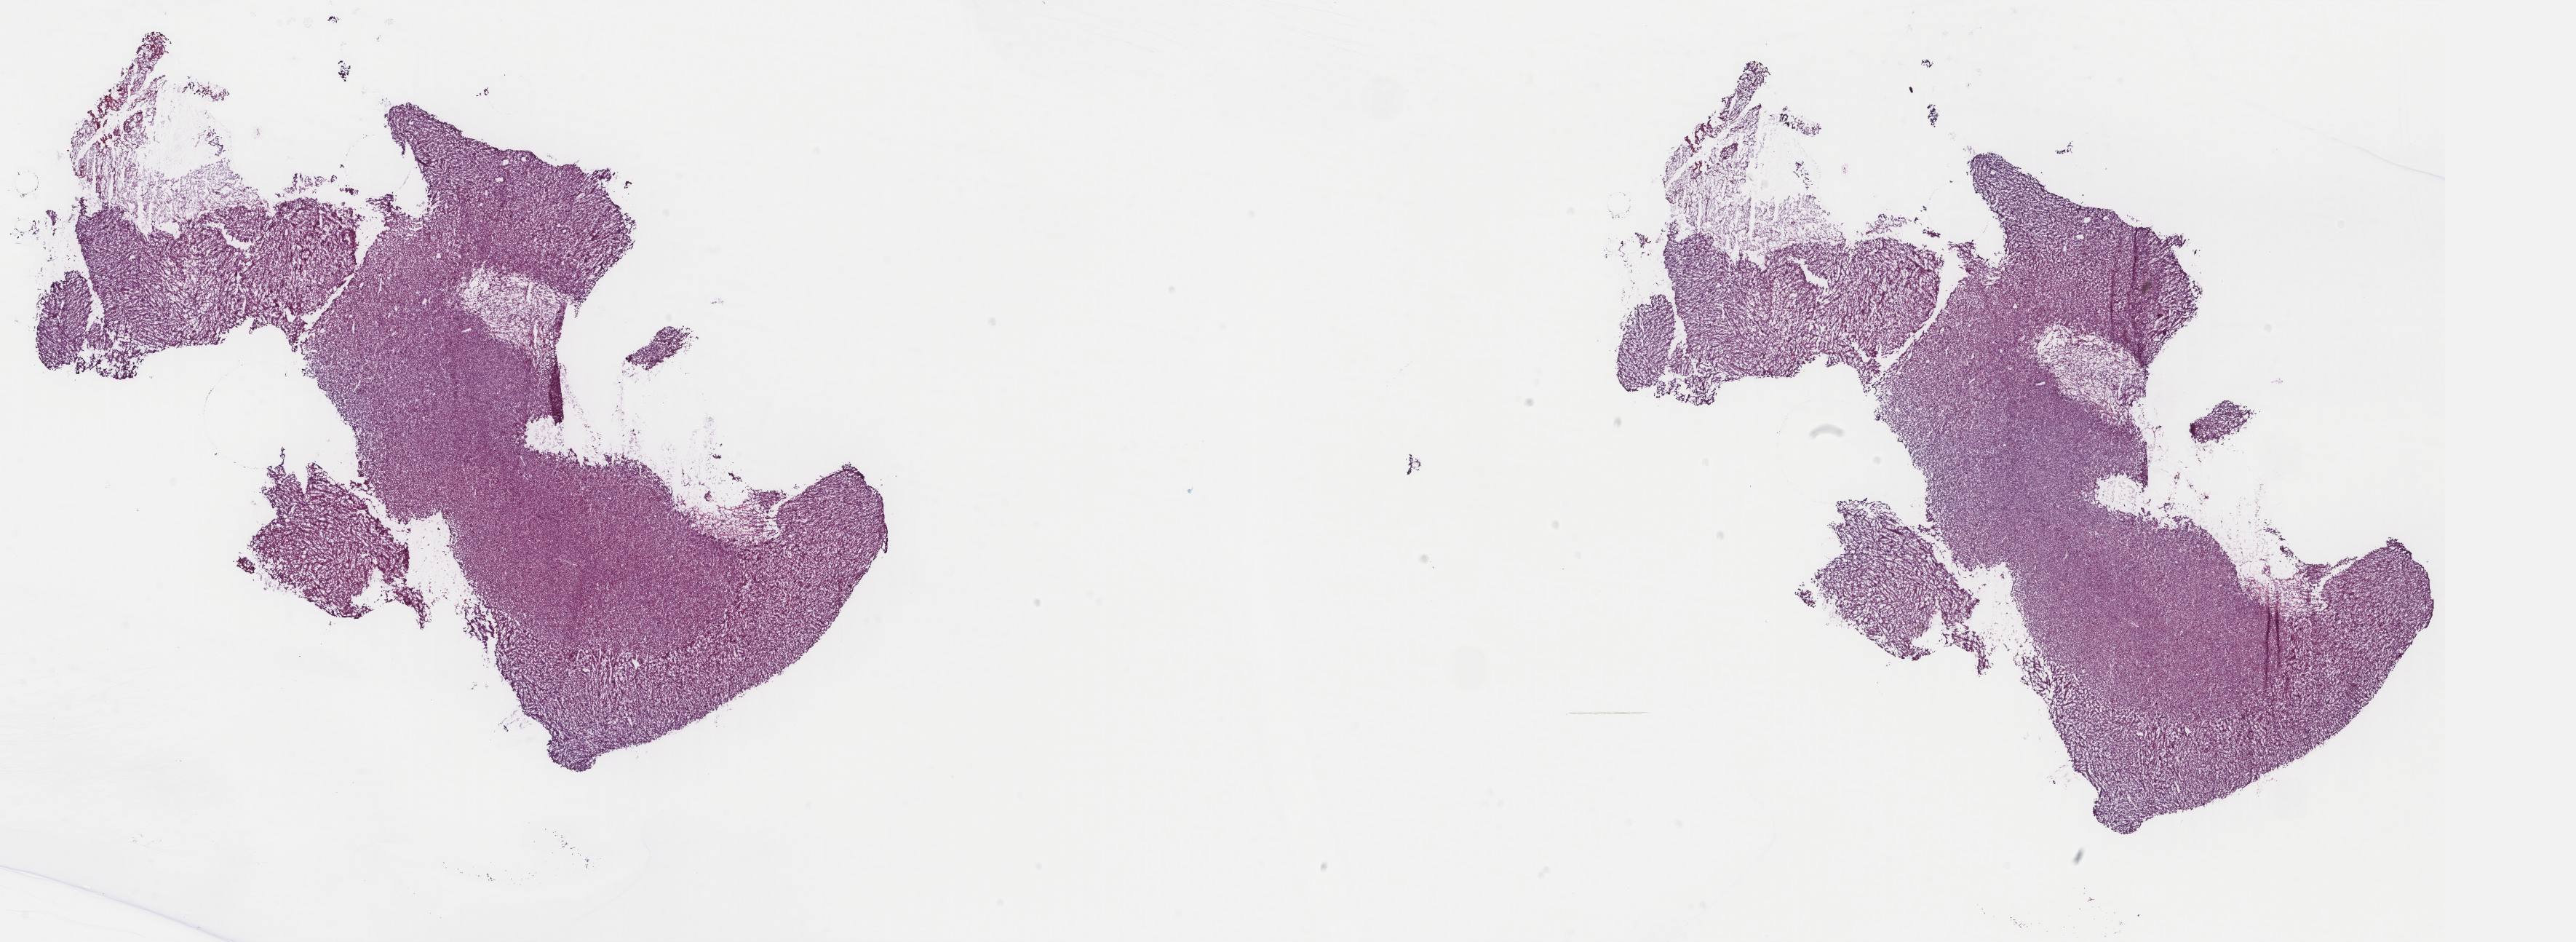
Whole-slide histology image, H&E, whole scanned area (about 28.1 x 10.3 mm) shown as a low-resolution overview, frozen section from the top of the tissue portion, sample: primary tumour, uterus. Female, age 65 years at initial diagnosis. Pathologist review of this section (percent, as recorded): tumour cells 85%, tumour nuclei 100%, normal cells 0%, stromal cells 10%, necrosis 5%. Infiltration values recorded for this section: lymphocyte infiltration 2%, monocyte infiltration 0%, neutrophil infiltration 0%.
- pathologic diagnosis: Leiomyosarcoma, NOS